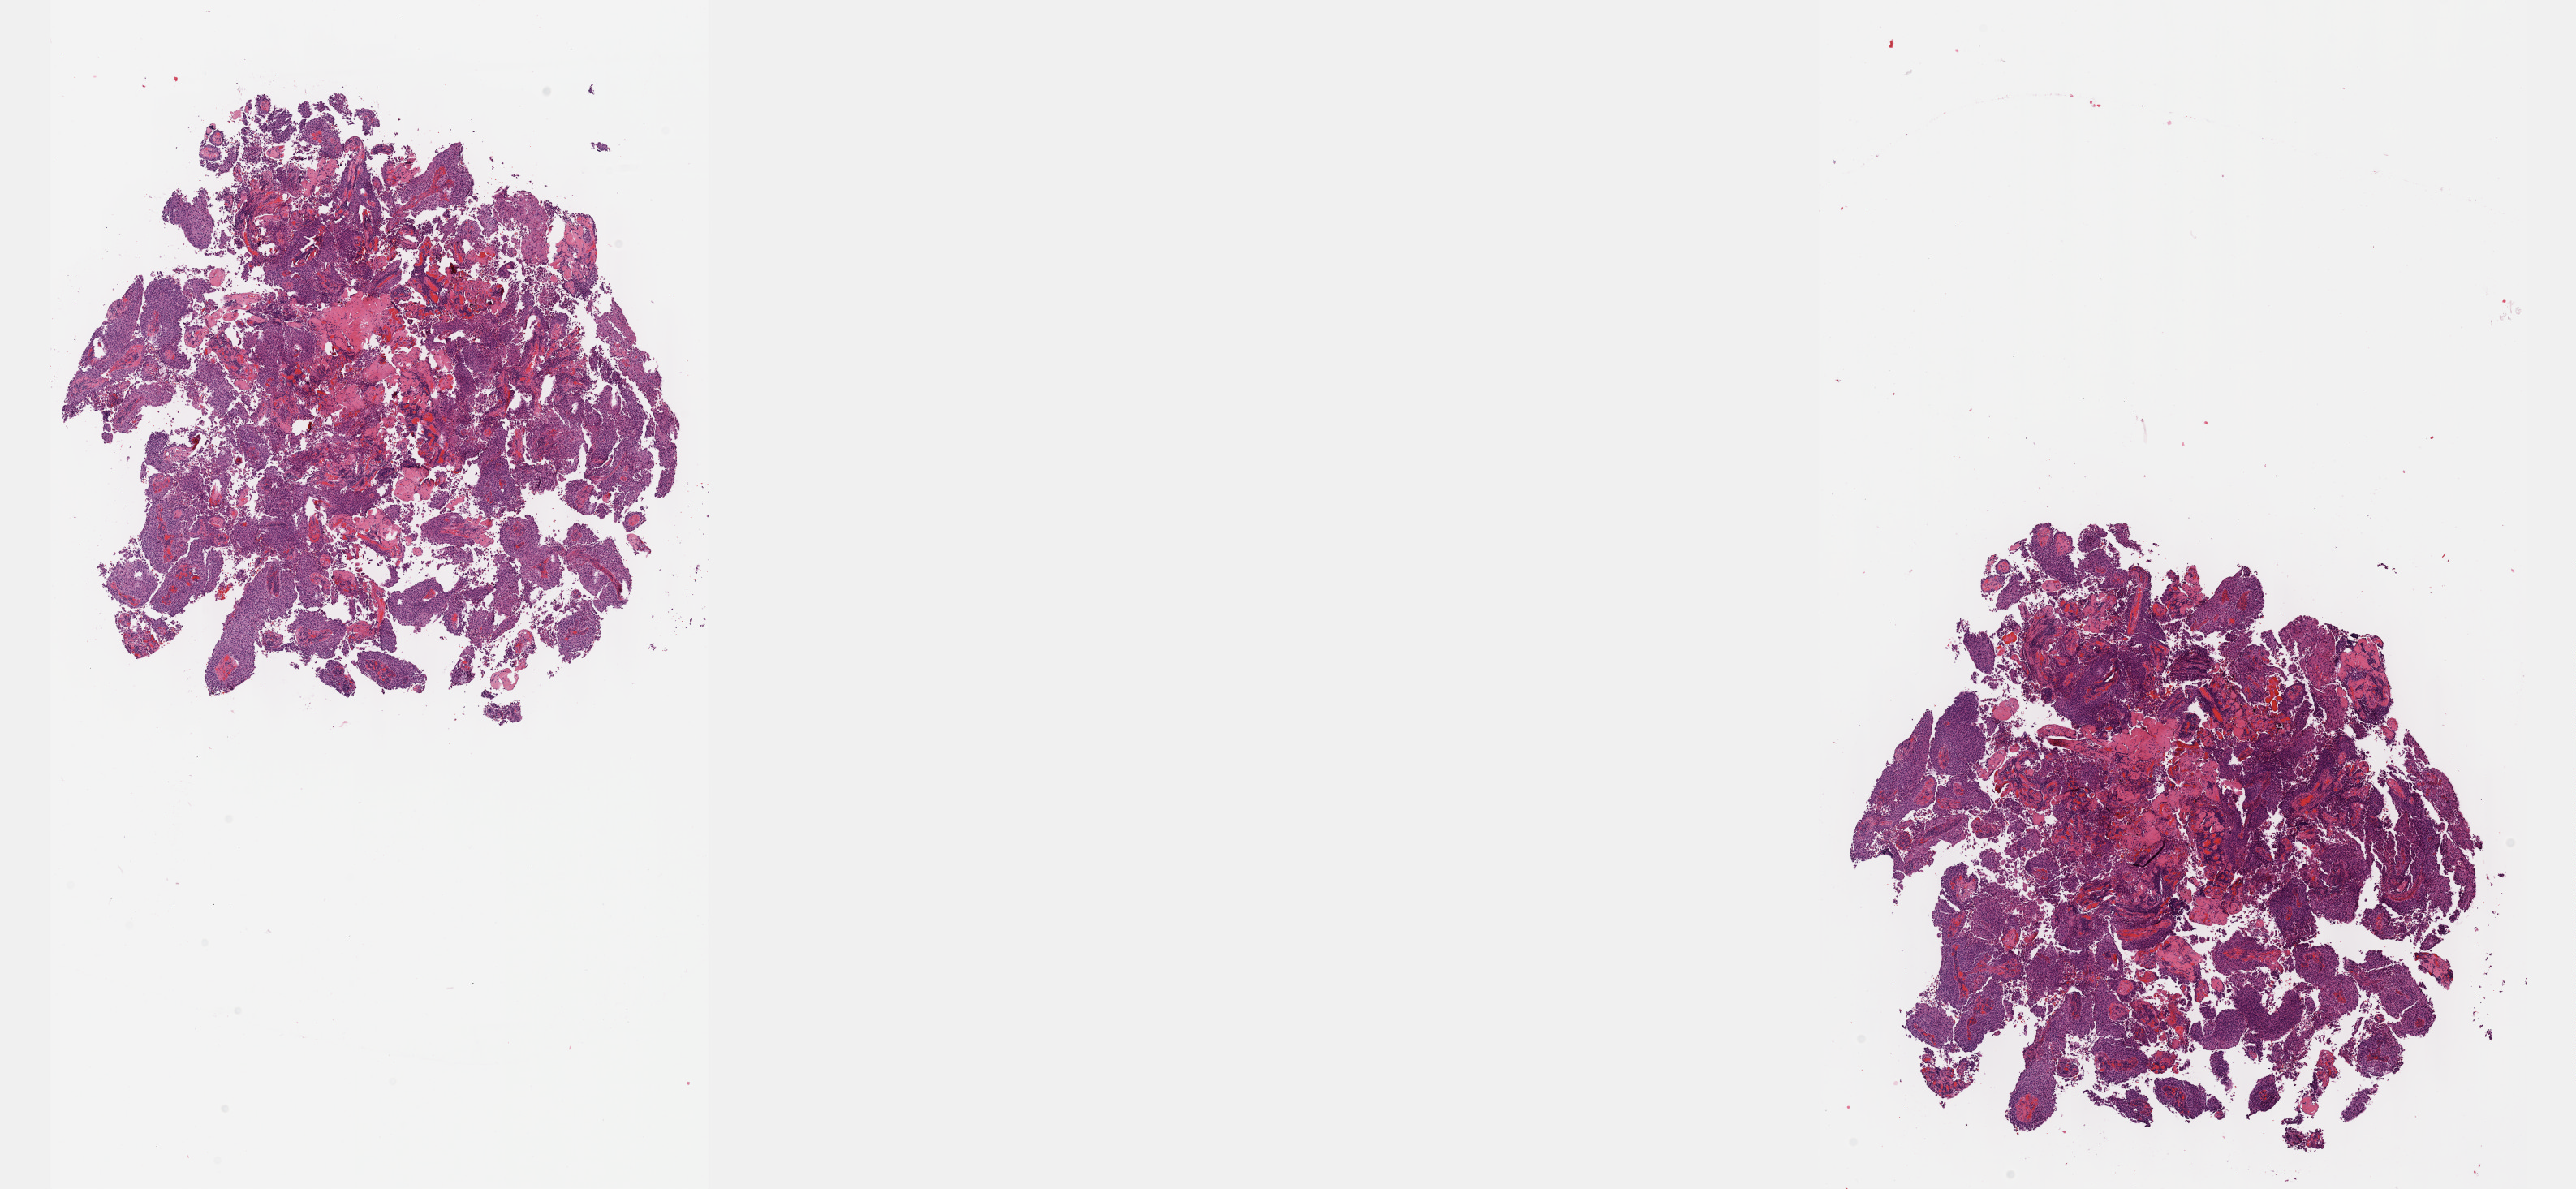
Whole-slide histology image, H&E-stained — shown as a low-resolution overview of the whole scanned area (about 25.7 x 11.8 mm, acquisition: 40x scan). Formalin-fixed paraffin-embedded (FFPE) diagnostic section. Bladder, primary tumour sample. Female patient; age at initial diagnosis 86 years.
Pathologic diagnosis: Transitional cell carcinoma.